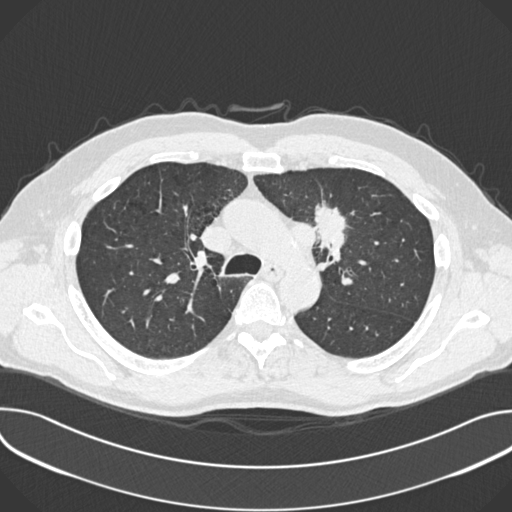
Low-dose screening chest CT, one axial slice; slice 259 of 361 in the series (ordered by position); reconstruction kernel B30f; lung window (W 1500 / L -600 HU); 1 mm slice thickness; 512 × 512 image matrix.
Structures marked on this image (expert manual segmentation):
- lesion 1 (tumor, upper lobe of left lung): box from (x=315, y=207) to (x=346, y=248) px